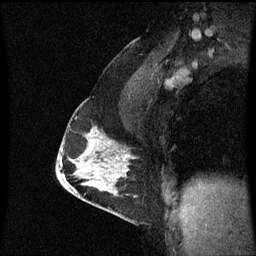
Breast MRI (dynamic contrast-enhanced), one sagittal slice. Position 38 of 60 along the scan axis. Dynamic contrast-enhanced series, image 2 of 3 at this slice position (ordered by acquisition). 1.5 T. TE 4.2 ms, TR 8.9 ms. 256 × 256 image matrix. Patient: female, 47 years. Case-level facts recorded for this patient, not image findings: setting: breast cancer imaged before/during neoadjuvant chemotherapy; receptor status: HR-positive, HER2-negative.
Outlined on this slice (semi-automatic segmentation, software-assisted and operator-edited):
- analysis volume of interest (the breast-tissue region the enhancement analysis was run in; not a lesion): bounding box (x1, y1, x2, y2) in pixels: (58, 110, 138, 209)
- tumour enhancement mask (voxels above the 70 % enhancement threshold inside the analysis volume of interest): (61, 134, 127, 191)